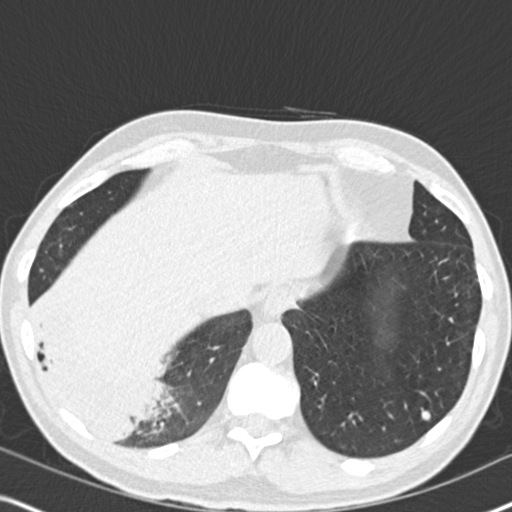
Low-dose screening chest CT, one axial slice; slice 52 of 182 in the series (ordered by position); 120 kVp; lung window (W 1500 / L -600 HU); 2 mm slice thickness; 512 × 512 image matrix, field of view 330 × 330 mm.
Annotated regions visible in this slice (expert manual segmentation):
- lesion 1 (tumor, lower lobe of right lung): bounding box [x1, y1, x2, y2] px = [47, 361, 160, 435]